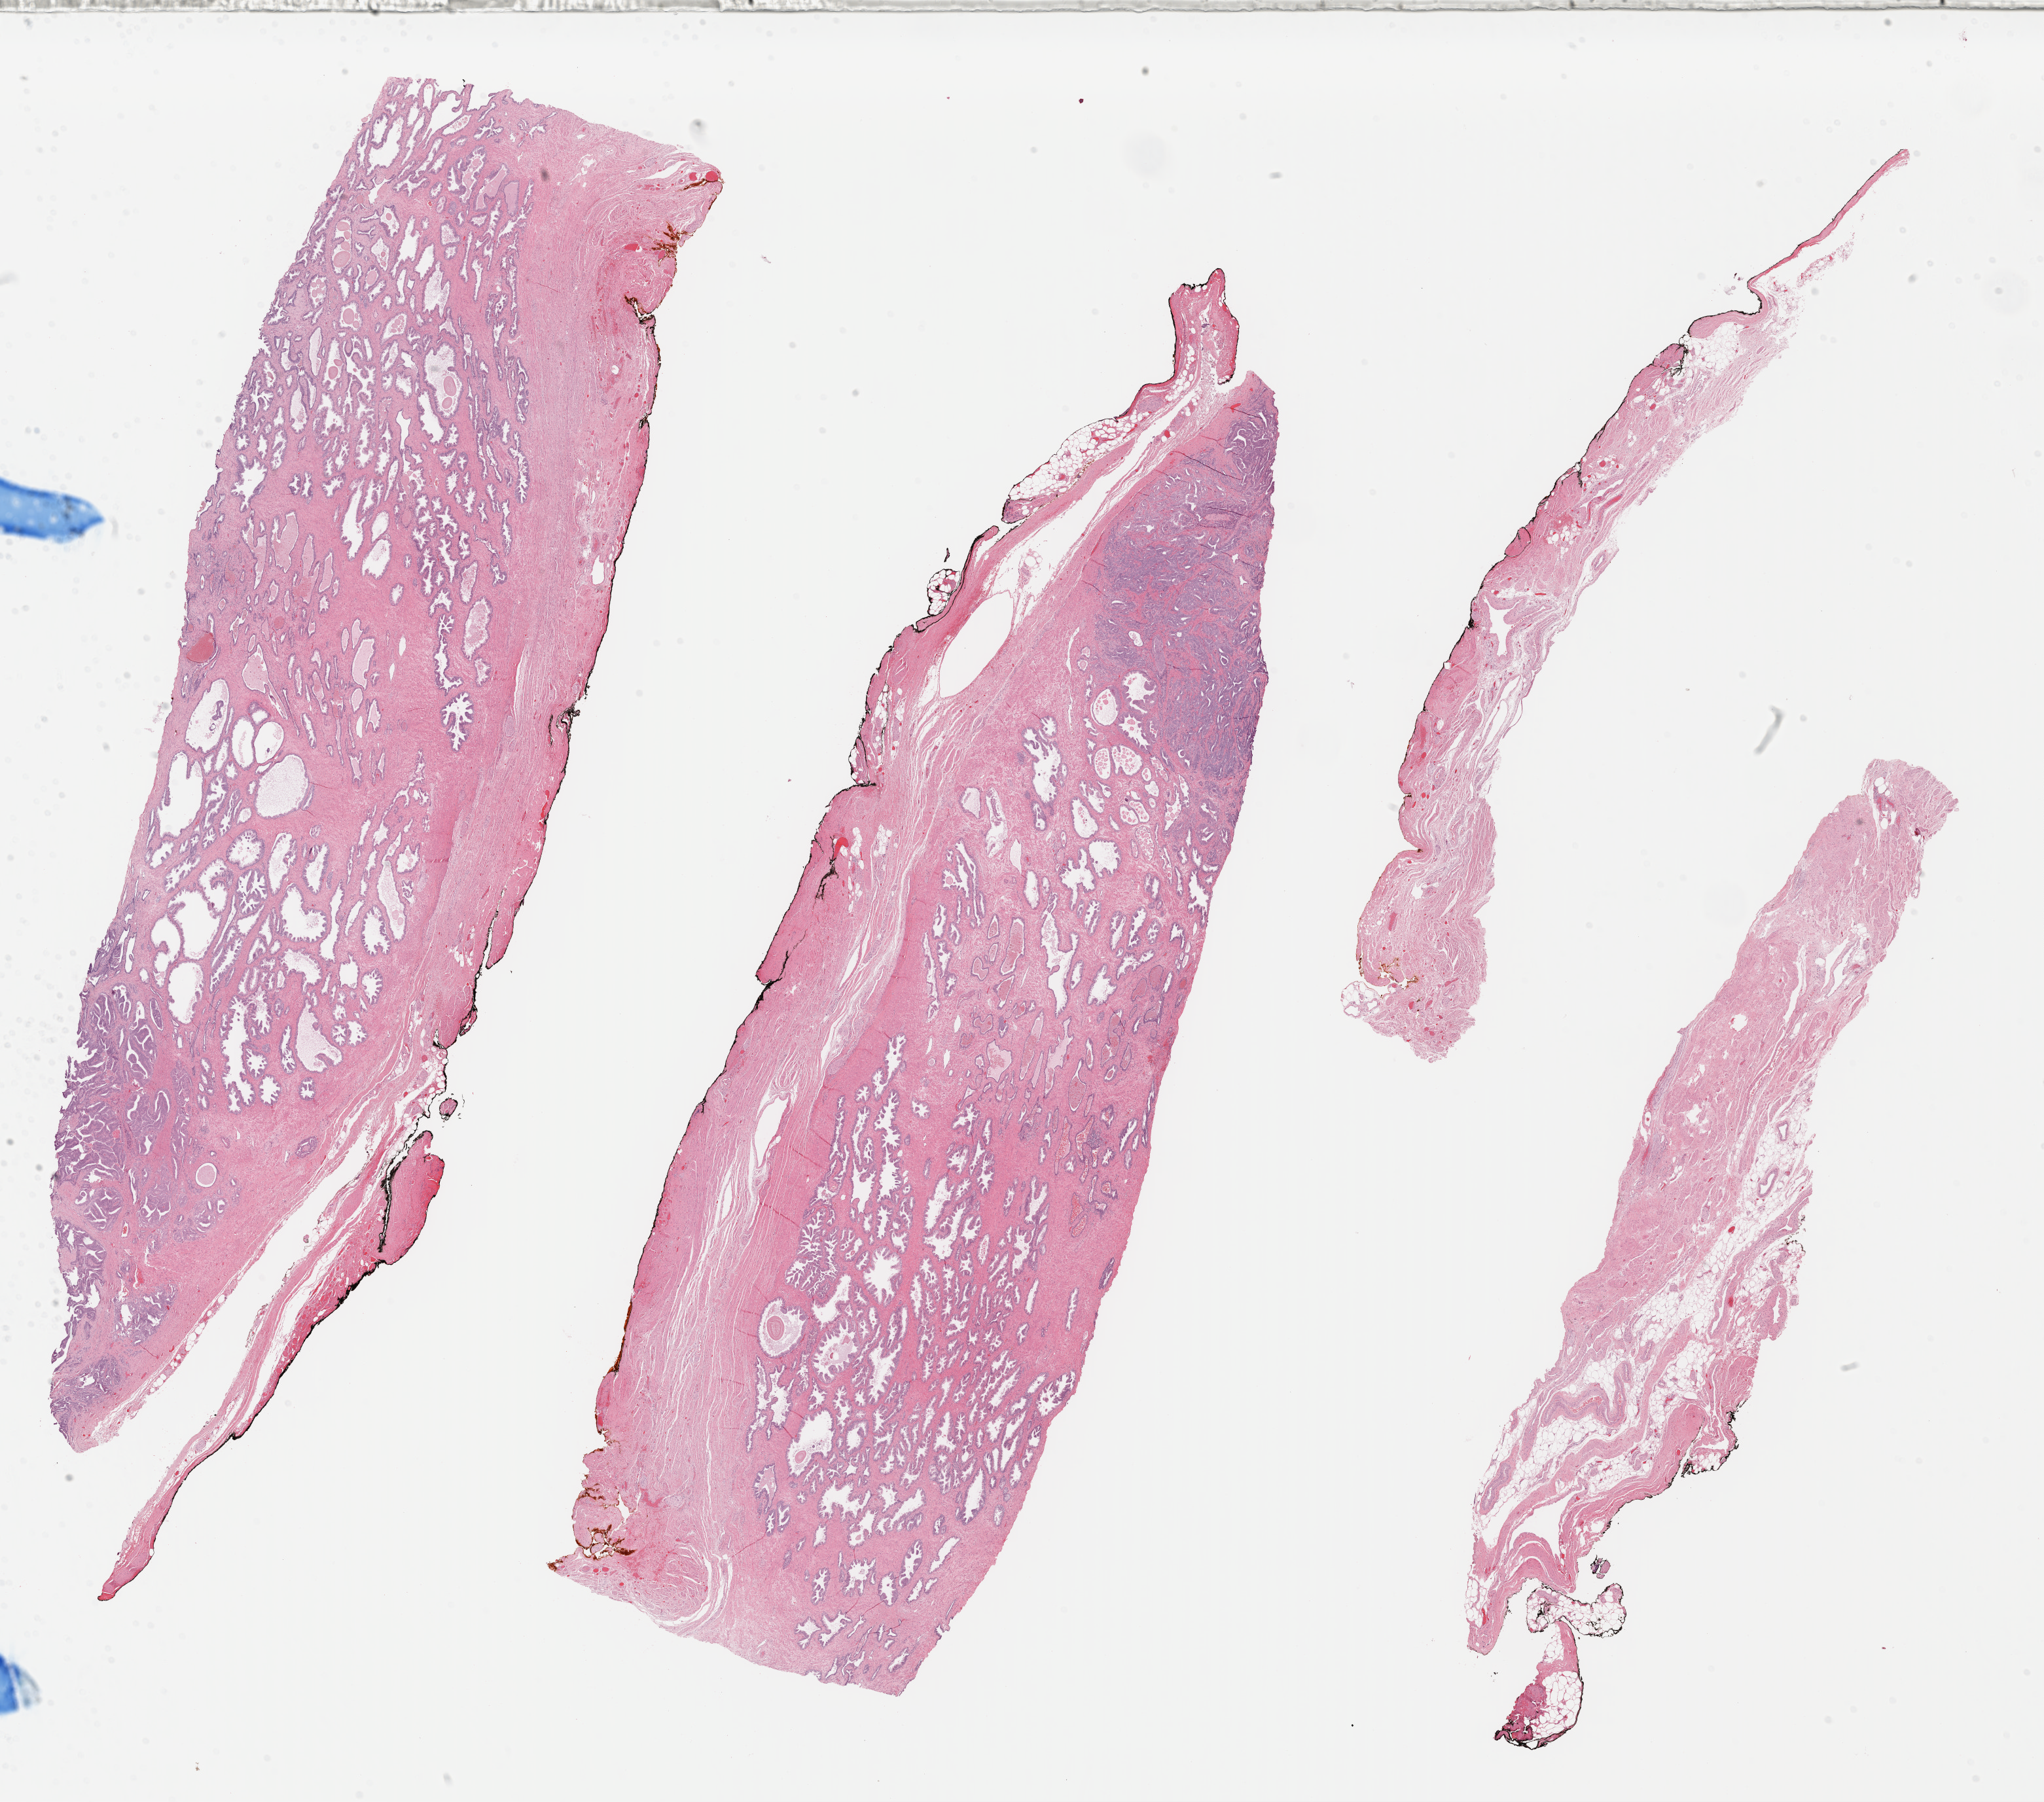
H&E whole-slide image, shown as a low-resolution overview of the whole scanned area (about 24.6 x 21.6 mm); formalin-fixed paraffin-embedded (FFPE) diagnostic section; sample: primary tumour, prostate. Patient: male, age at initial diagnosis 71 years.
Pathologic diagnosis: Infiltrating duct carcinoma, NOS (prostate gland).